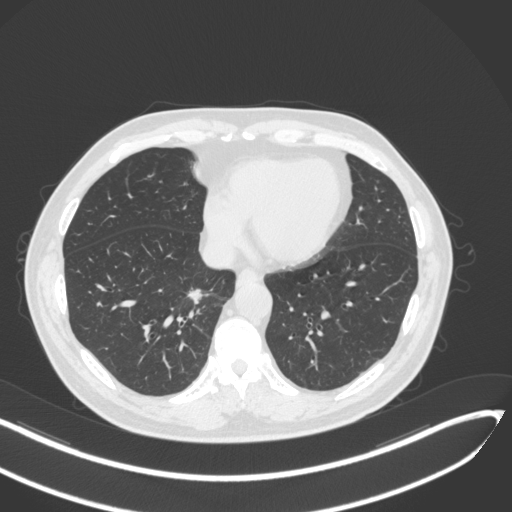
Chest CT, one axial slice. Position 122 of 429 along the scan axis. Lung window (W 1500 / L -600 HU). 1 mm slice thickness. 512 × 512 image matrix. Male patient, age 62 years. Case-level facts recorded for this patient, not image findings: clinical TNM (as recorded): T1b N0 M0; histopathological grade: G2.
Outlined on this slice (bounding box drawn by a radiologist):
- lung tumour (recorded histology: adenocarcinoma): box from (x=187, y=286) to (x=220, y=309) px